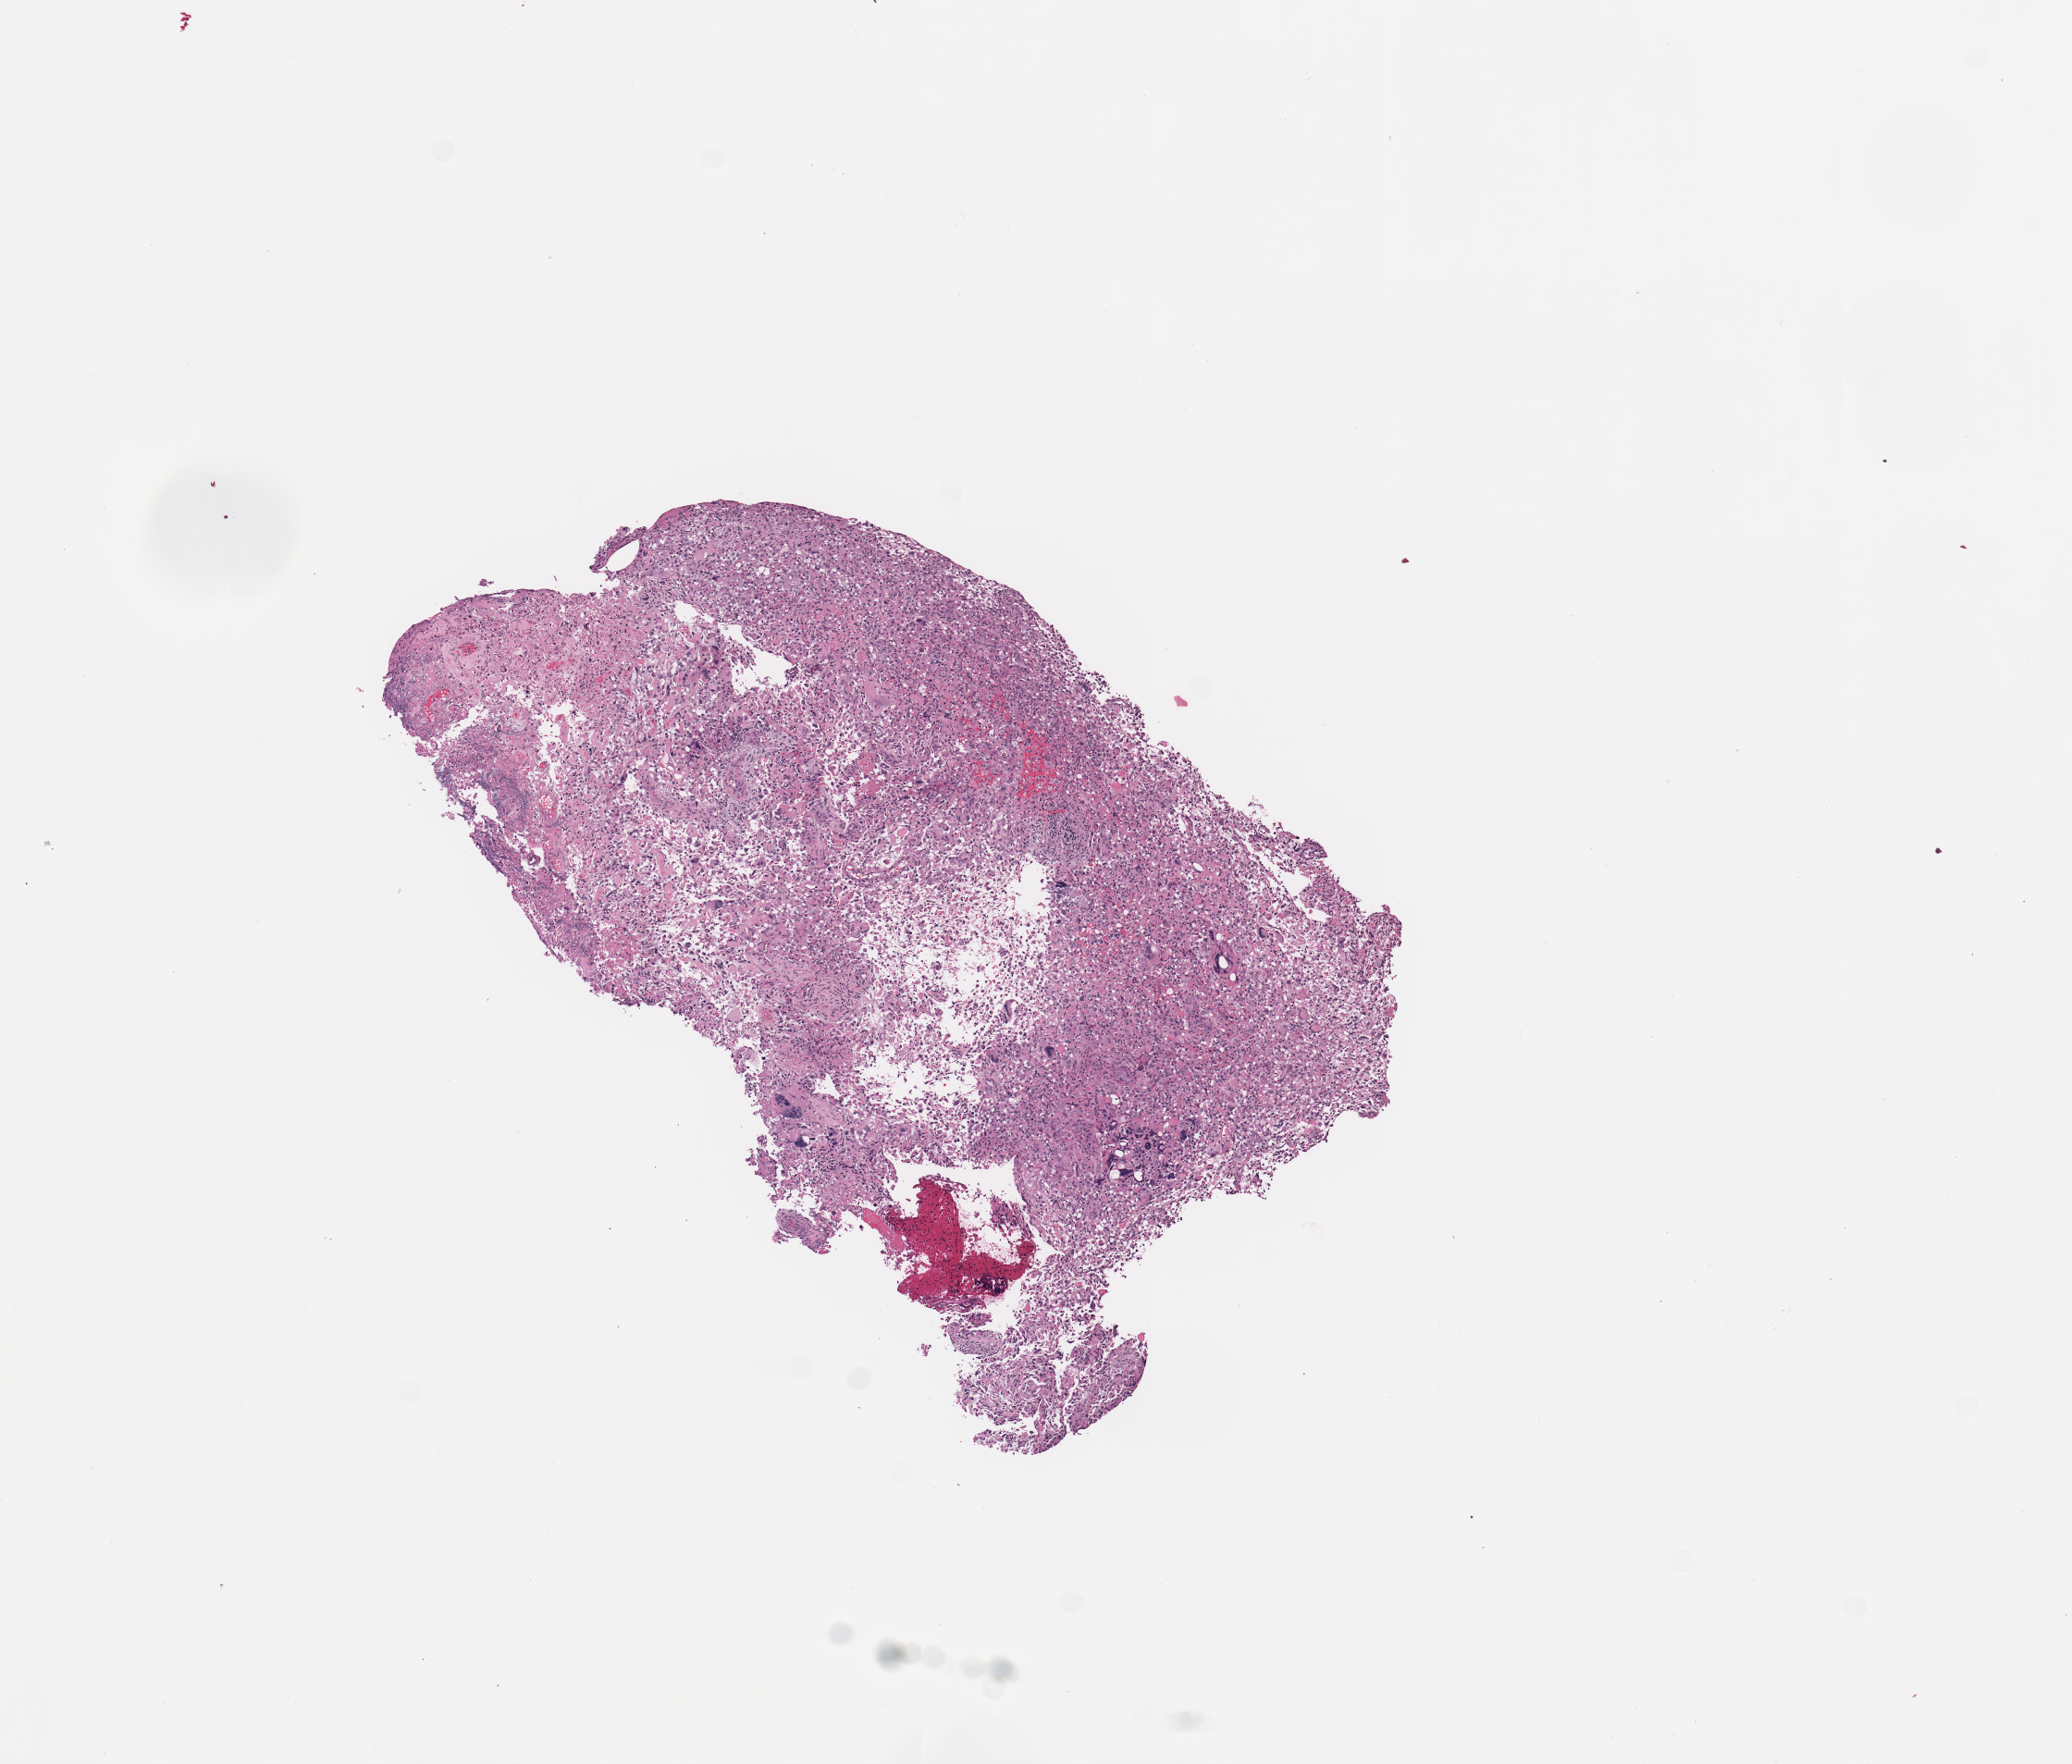
H&E whole-slide image, a low-resolution overview of the entire scanned area, about 8.9 x 7.5 mm (acquisition: 20x scan). Tumour tissue sample, sampled site: brain. Female, 38 y/o. Composition of this section per pathologist review: tumour nuclei 75%, necrosis 7%.
Histologic diagnosis: Glioblastoma.